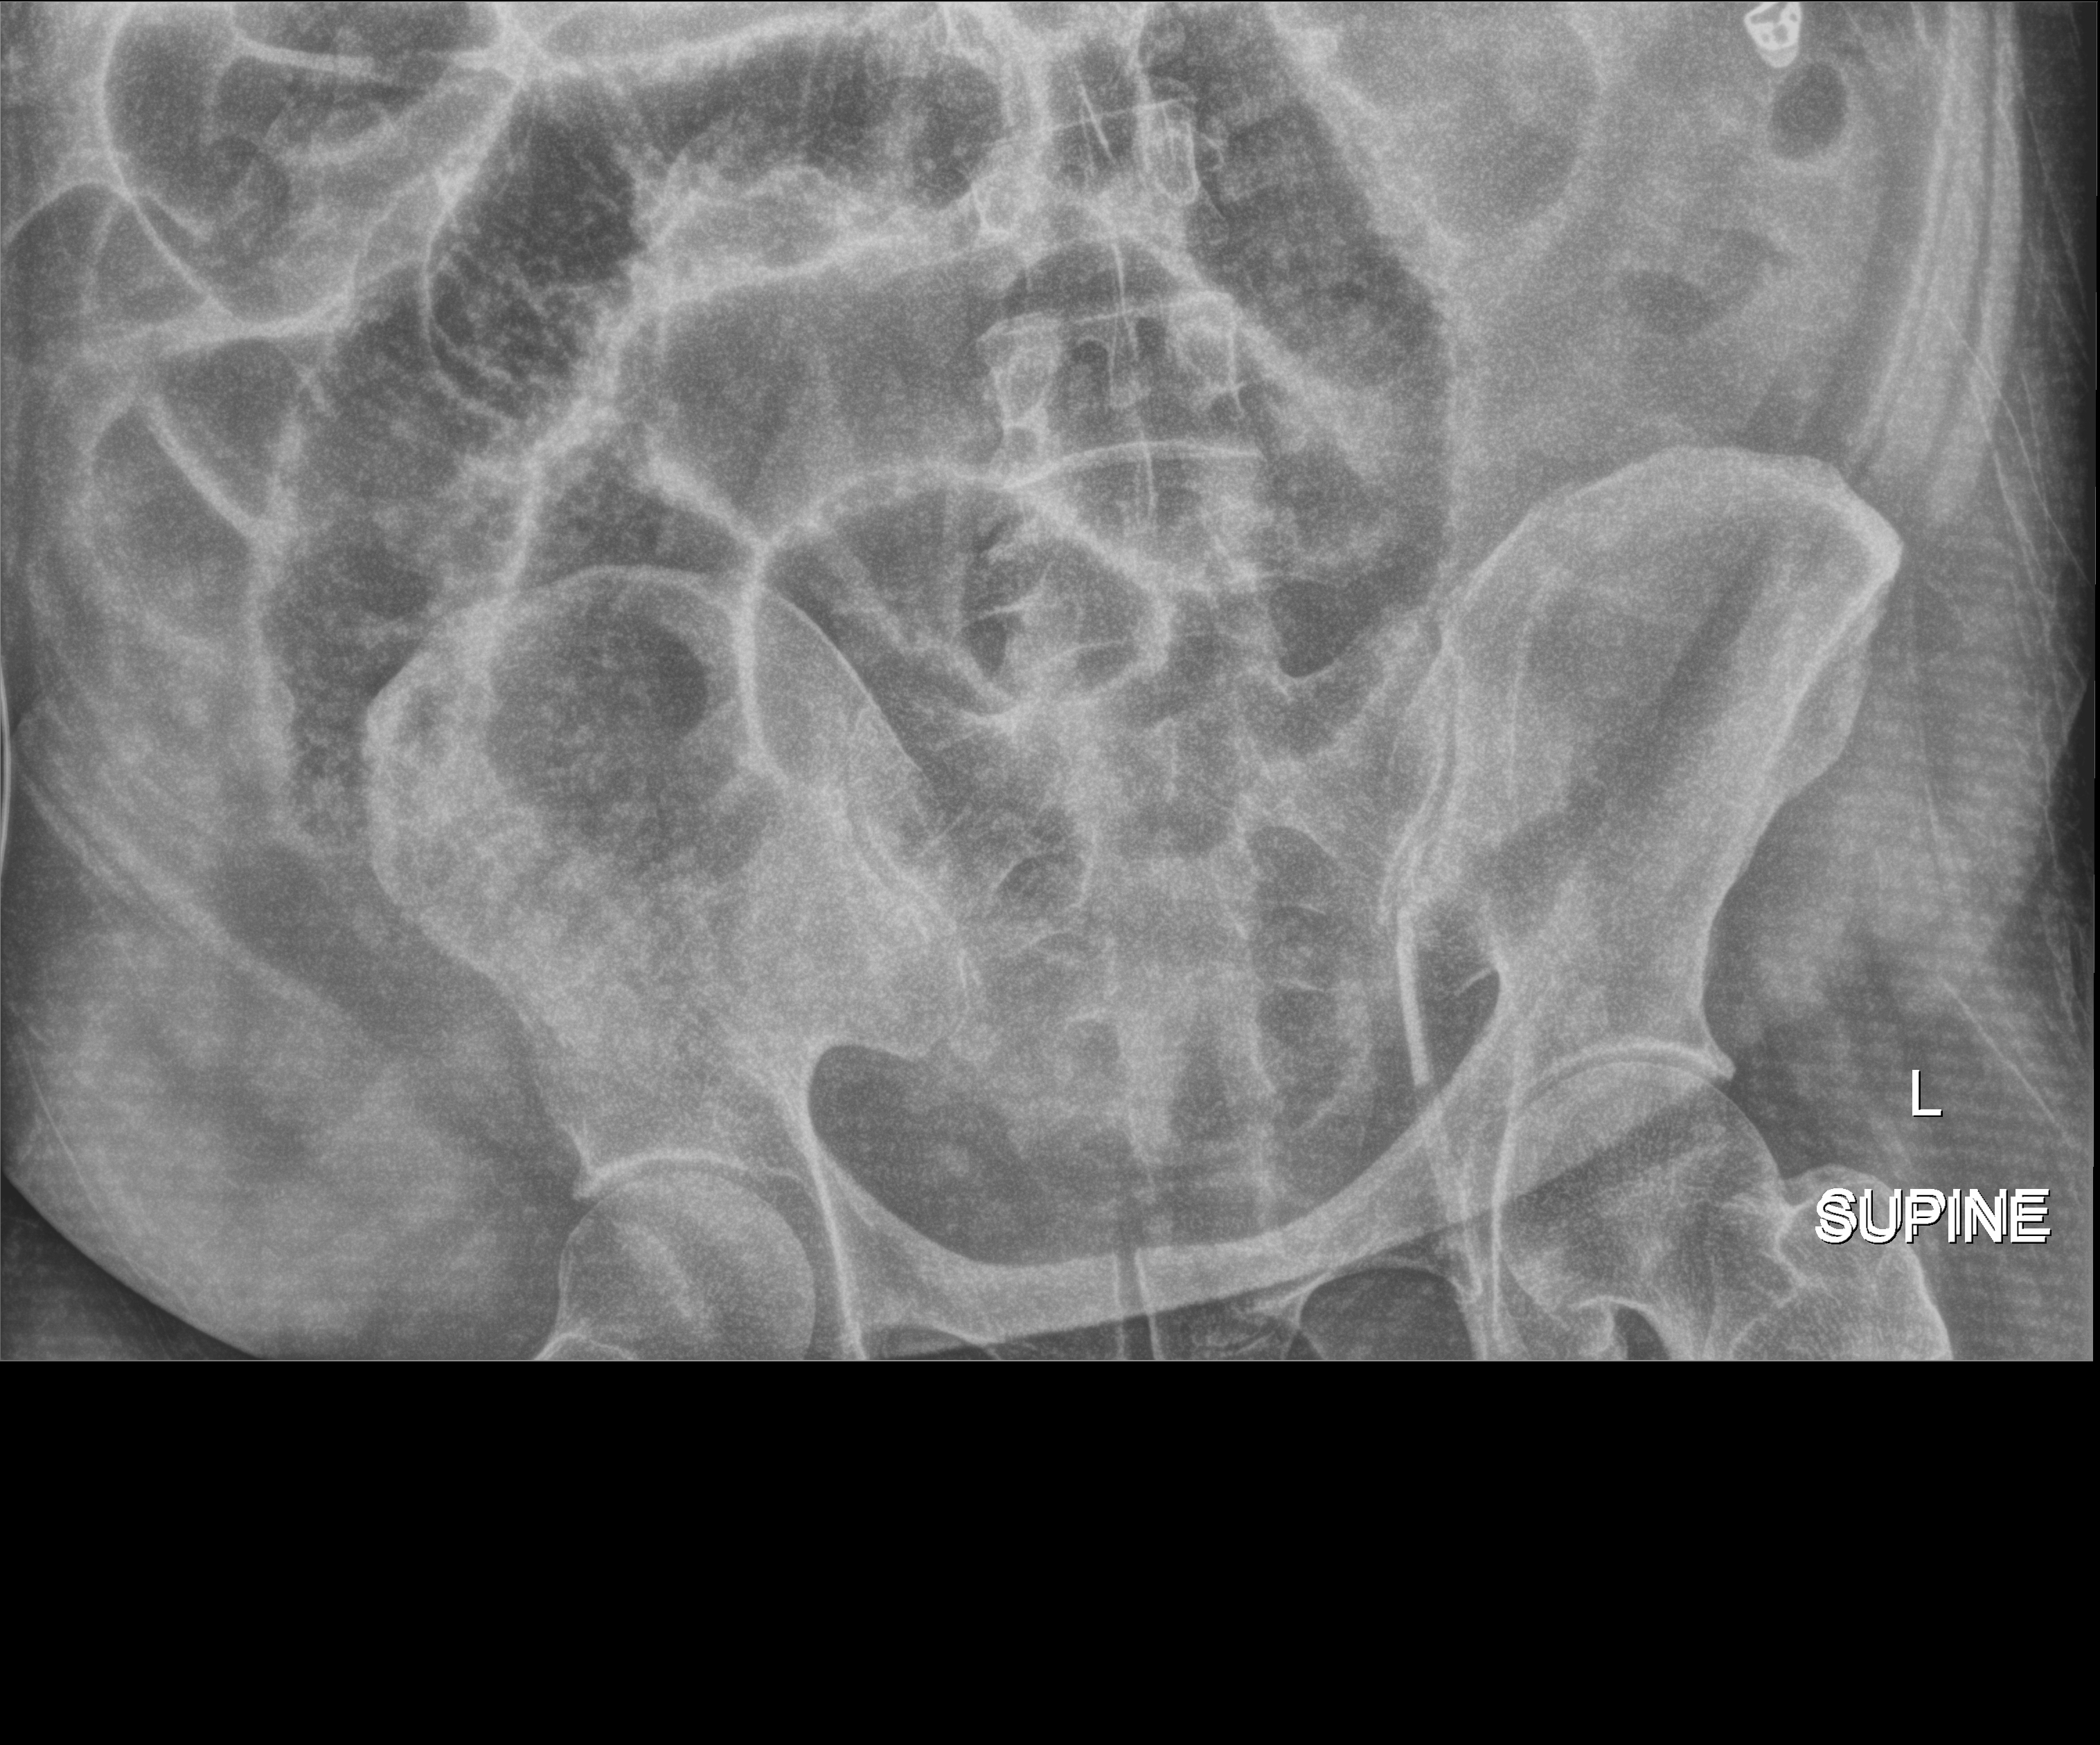
Abdomen X-ray (portable); anteroposterior (AP) projection. Patient hospitalised with COVID-19, aged 18–59 years.
Admission-level facts for this patient (not findings on this image; timing relative to this image not recorded): admitted to intensive care during this hospital stay: yes.